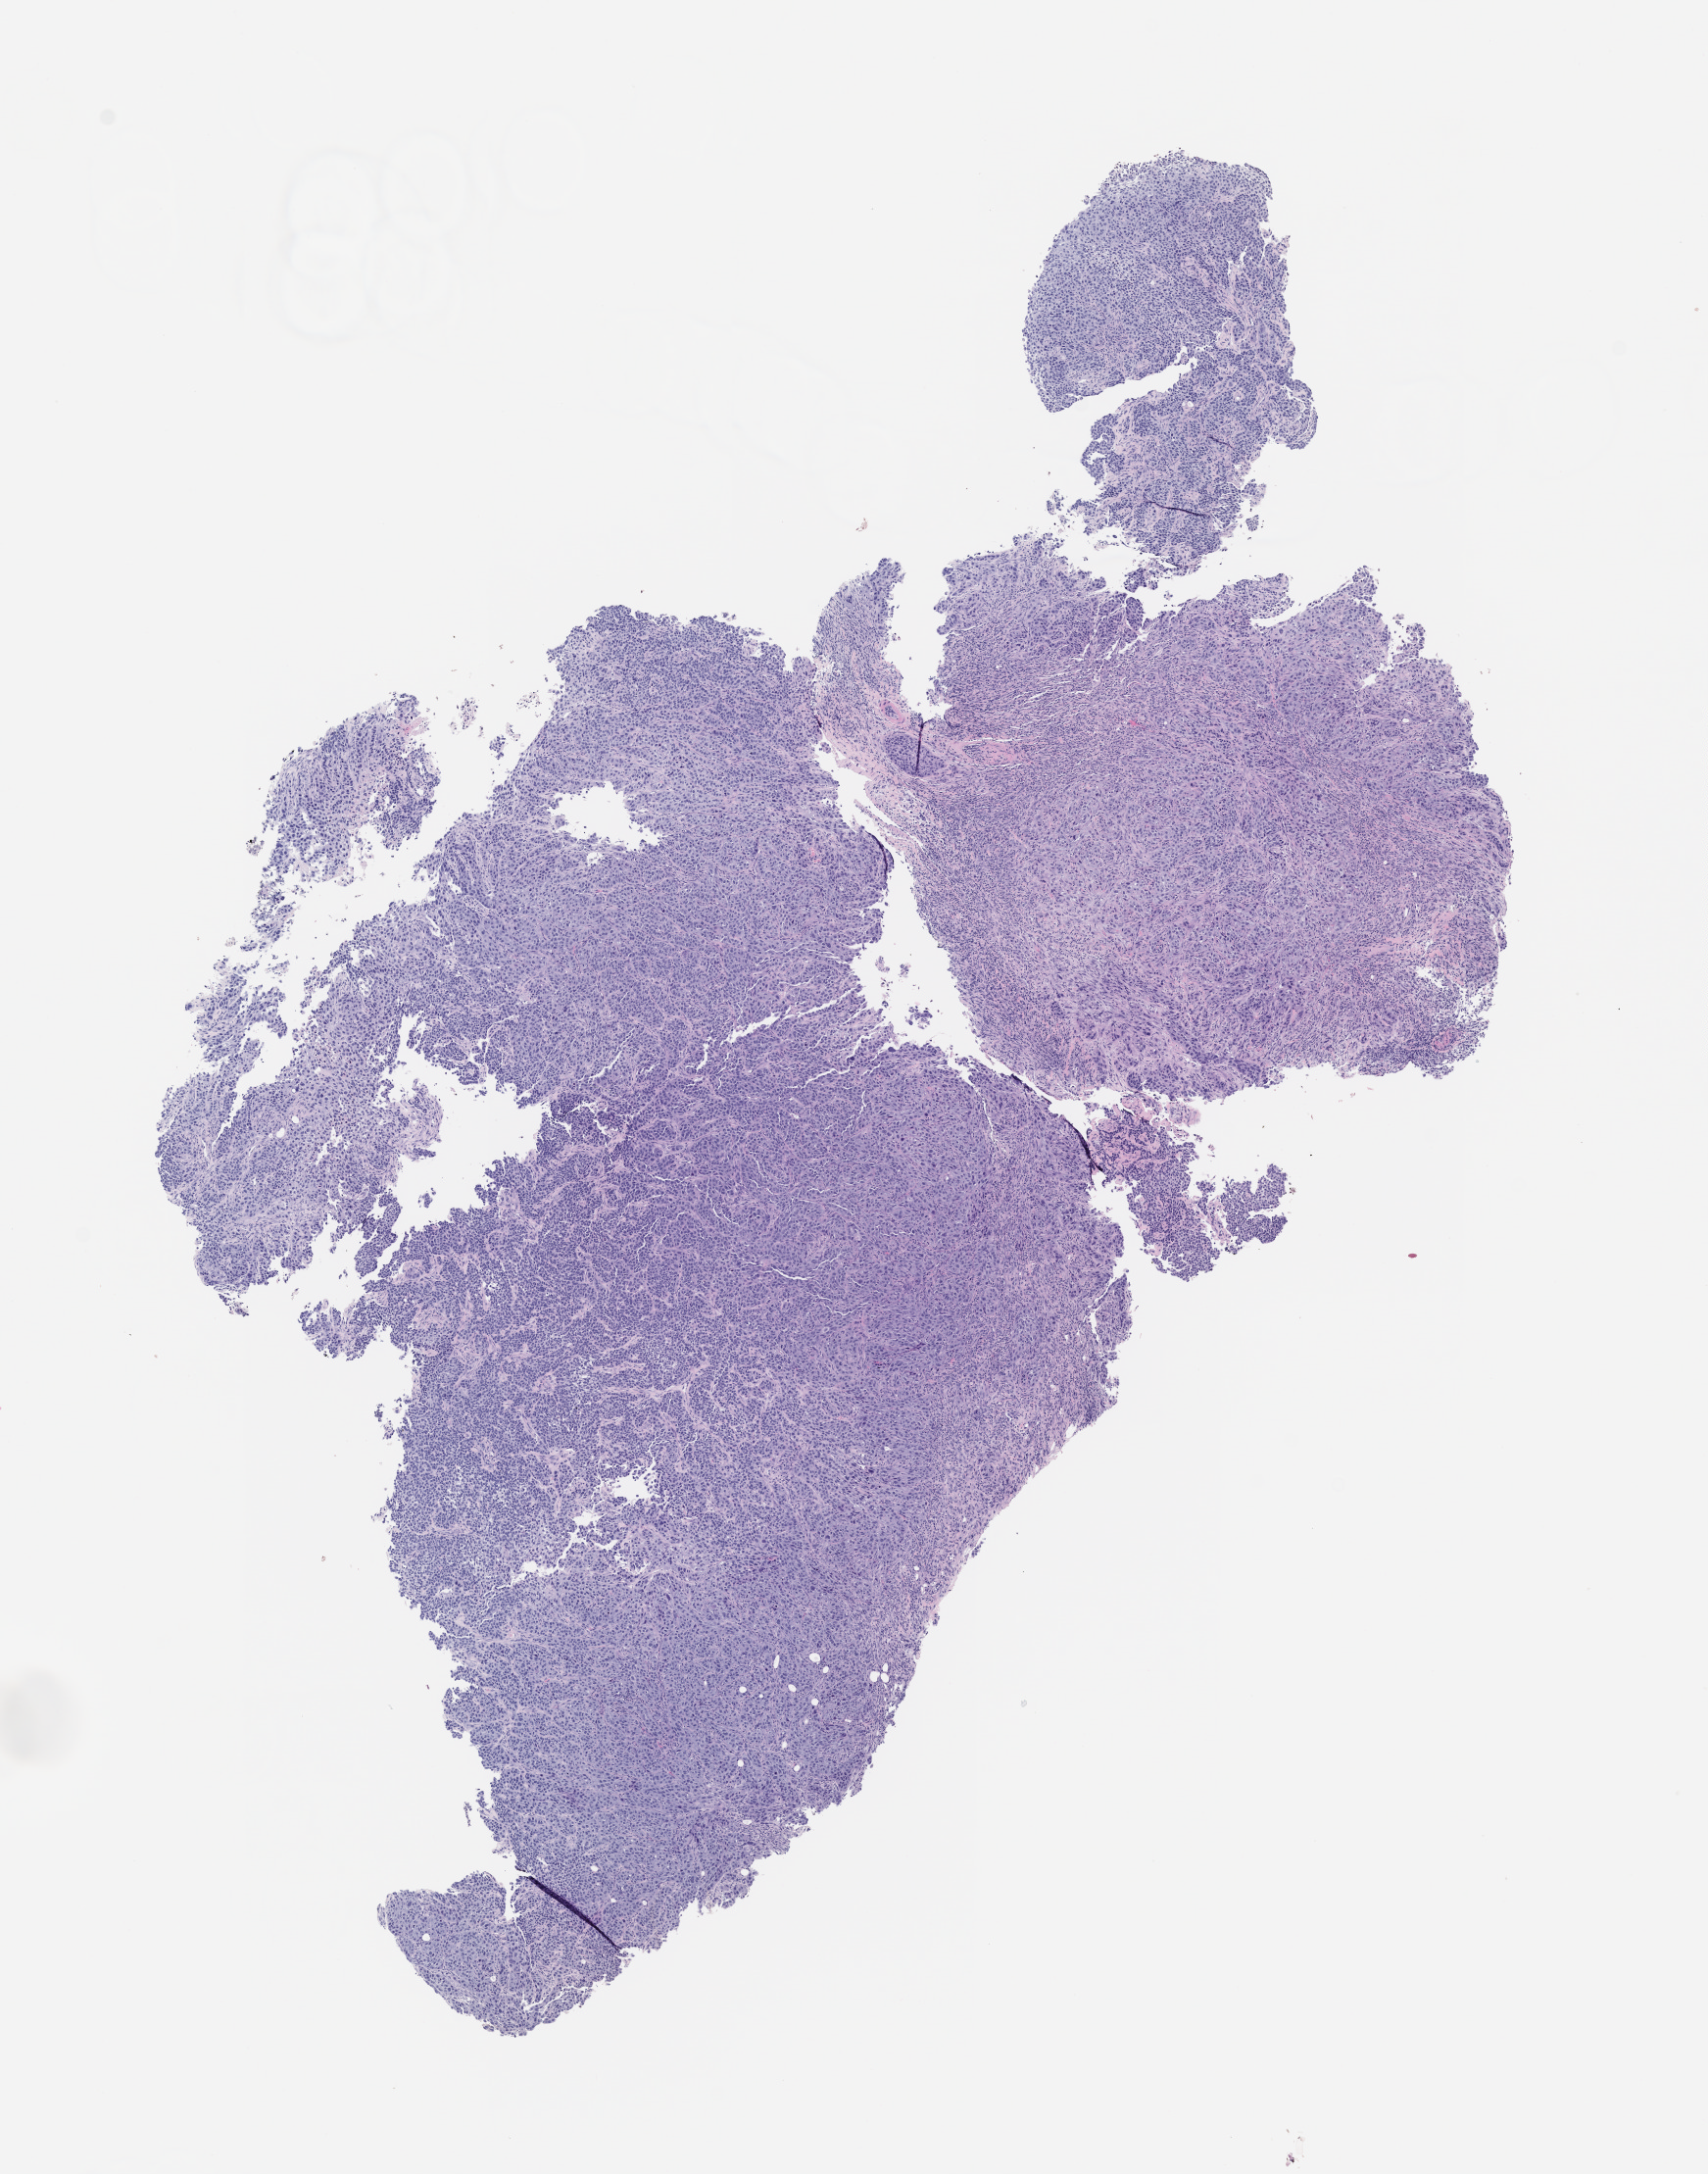
Whole-slide image, hematoxylin and eosin (H&E): patient-derived xenograft (human tumor grown in a mouse), passage 3 — low-resolution overview of the scanned area, about 7.0 x 8.9 mm; formalin-fixed, paraffin-embedded (FFPE) tissue; originating tumor site category: bladder.
Originating patient diagnosis: Transitional Cell Carcinoma.